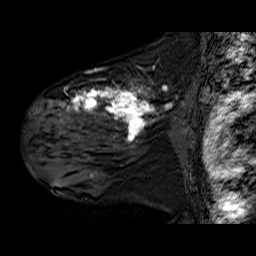
Breast MRI (dynamic contrast-enhanced), one sagittal slice; slice 43 of 60 in the series (ordered by position); dynamic contrast-enhanced series, time point 2 of 6 at this slice position (early post-contrast); 1.5 T; TE 6.3 ms, TR 32.9 ms; 4 mm slice thickness; 256 × 256 image matrix. Female patient. Case-level facts recorded for this patient, not image findings: setting: breast cancer imaged before/during neoadjuvant chemotherapy; receptor status: HER2-positive.
Annotated regions visible in this slice (semi-automatically segmented with operator editing):
- analysis volume of interest (the breast-tissue region the enhancement analysis was run in; not a lesion): bounding box (x1, y1, x2, y2) in pixels: (30, 78, 180, 180)
- tumour enhancement mask (voxels above the 100 % enhancement threshold inside the analysis volume of interest): (51, 84, 171, 178)